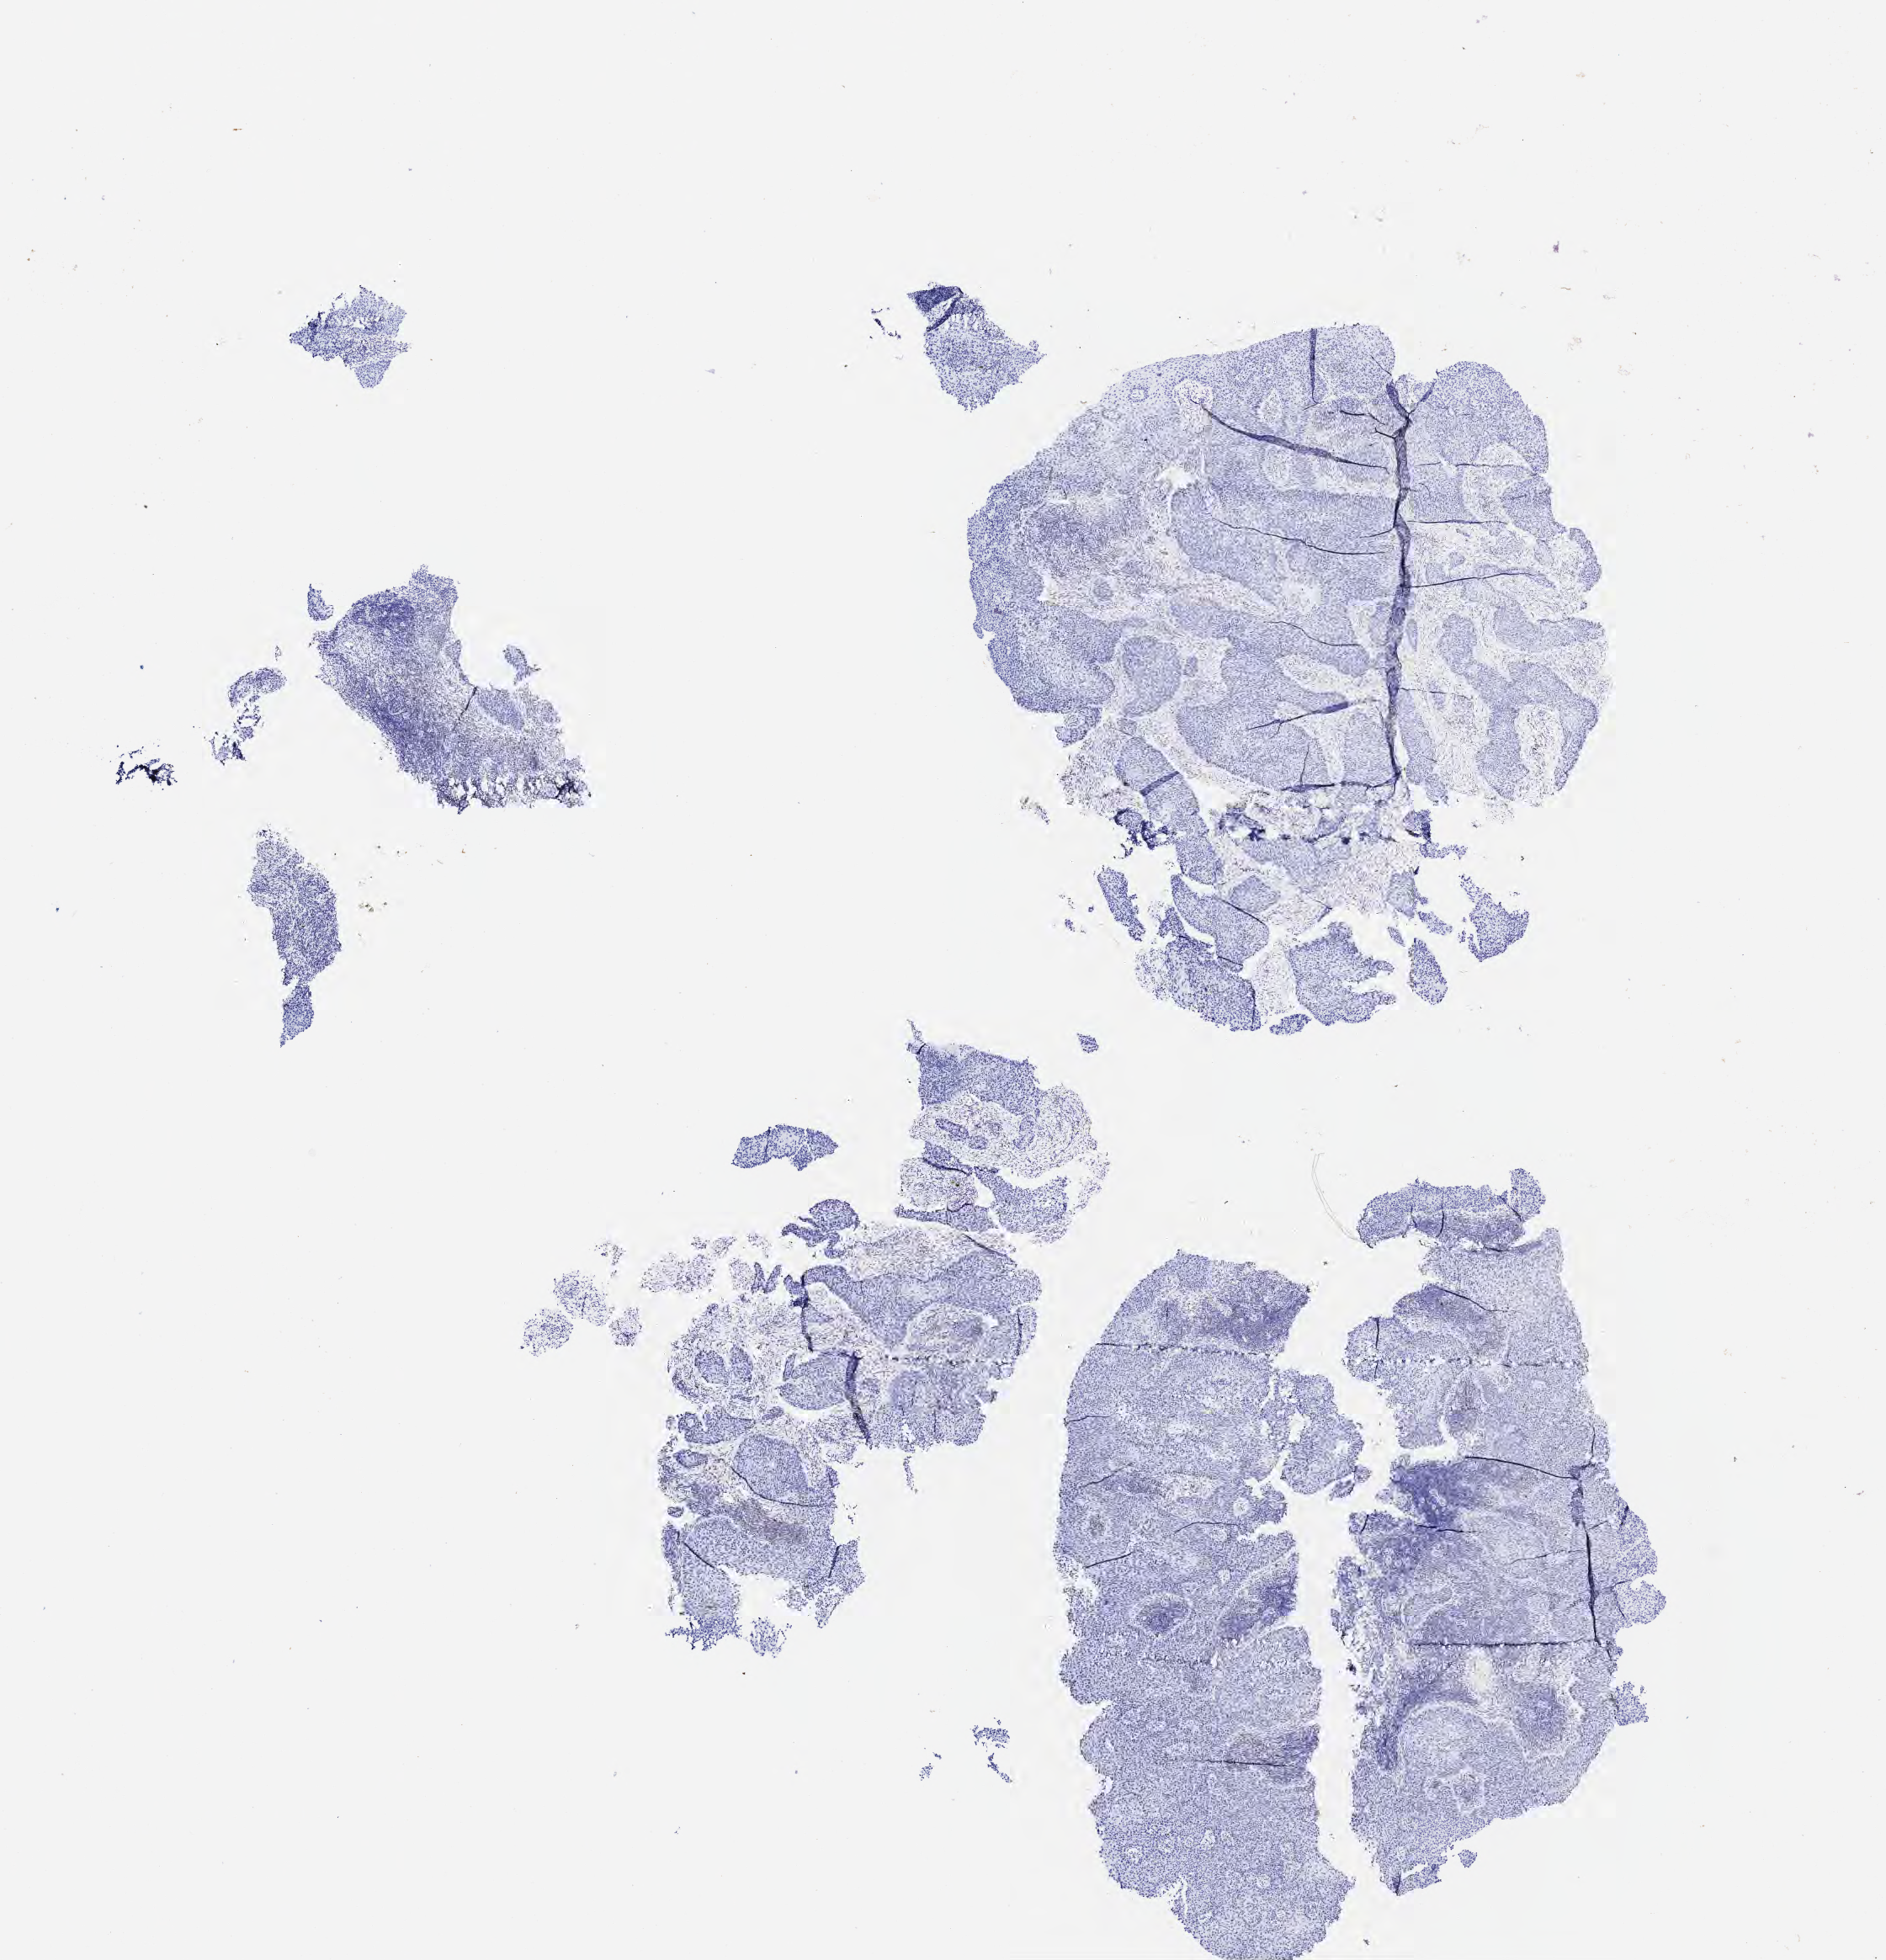
IHC for p16 (p16INK4a), whole-slide image, shown as a low-resolution overview of the whole scanned area (about 9.1 x 9.4 mm), specimen: tumor tissue, site: cervix. Female patient, aged 49.
* diagnosis: Squamous cell carcinoma, large cell, nonkeratinizing, NOS